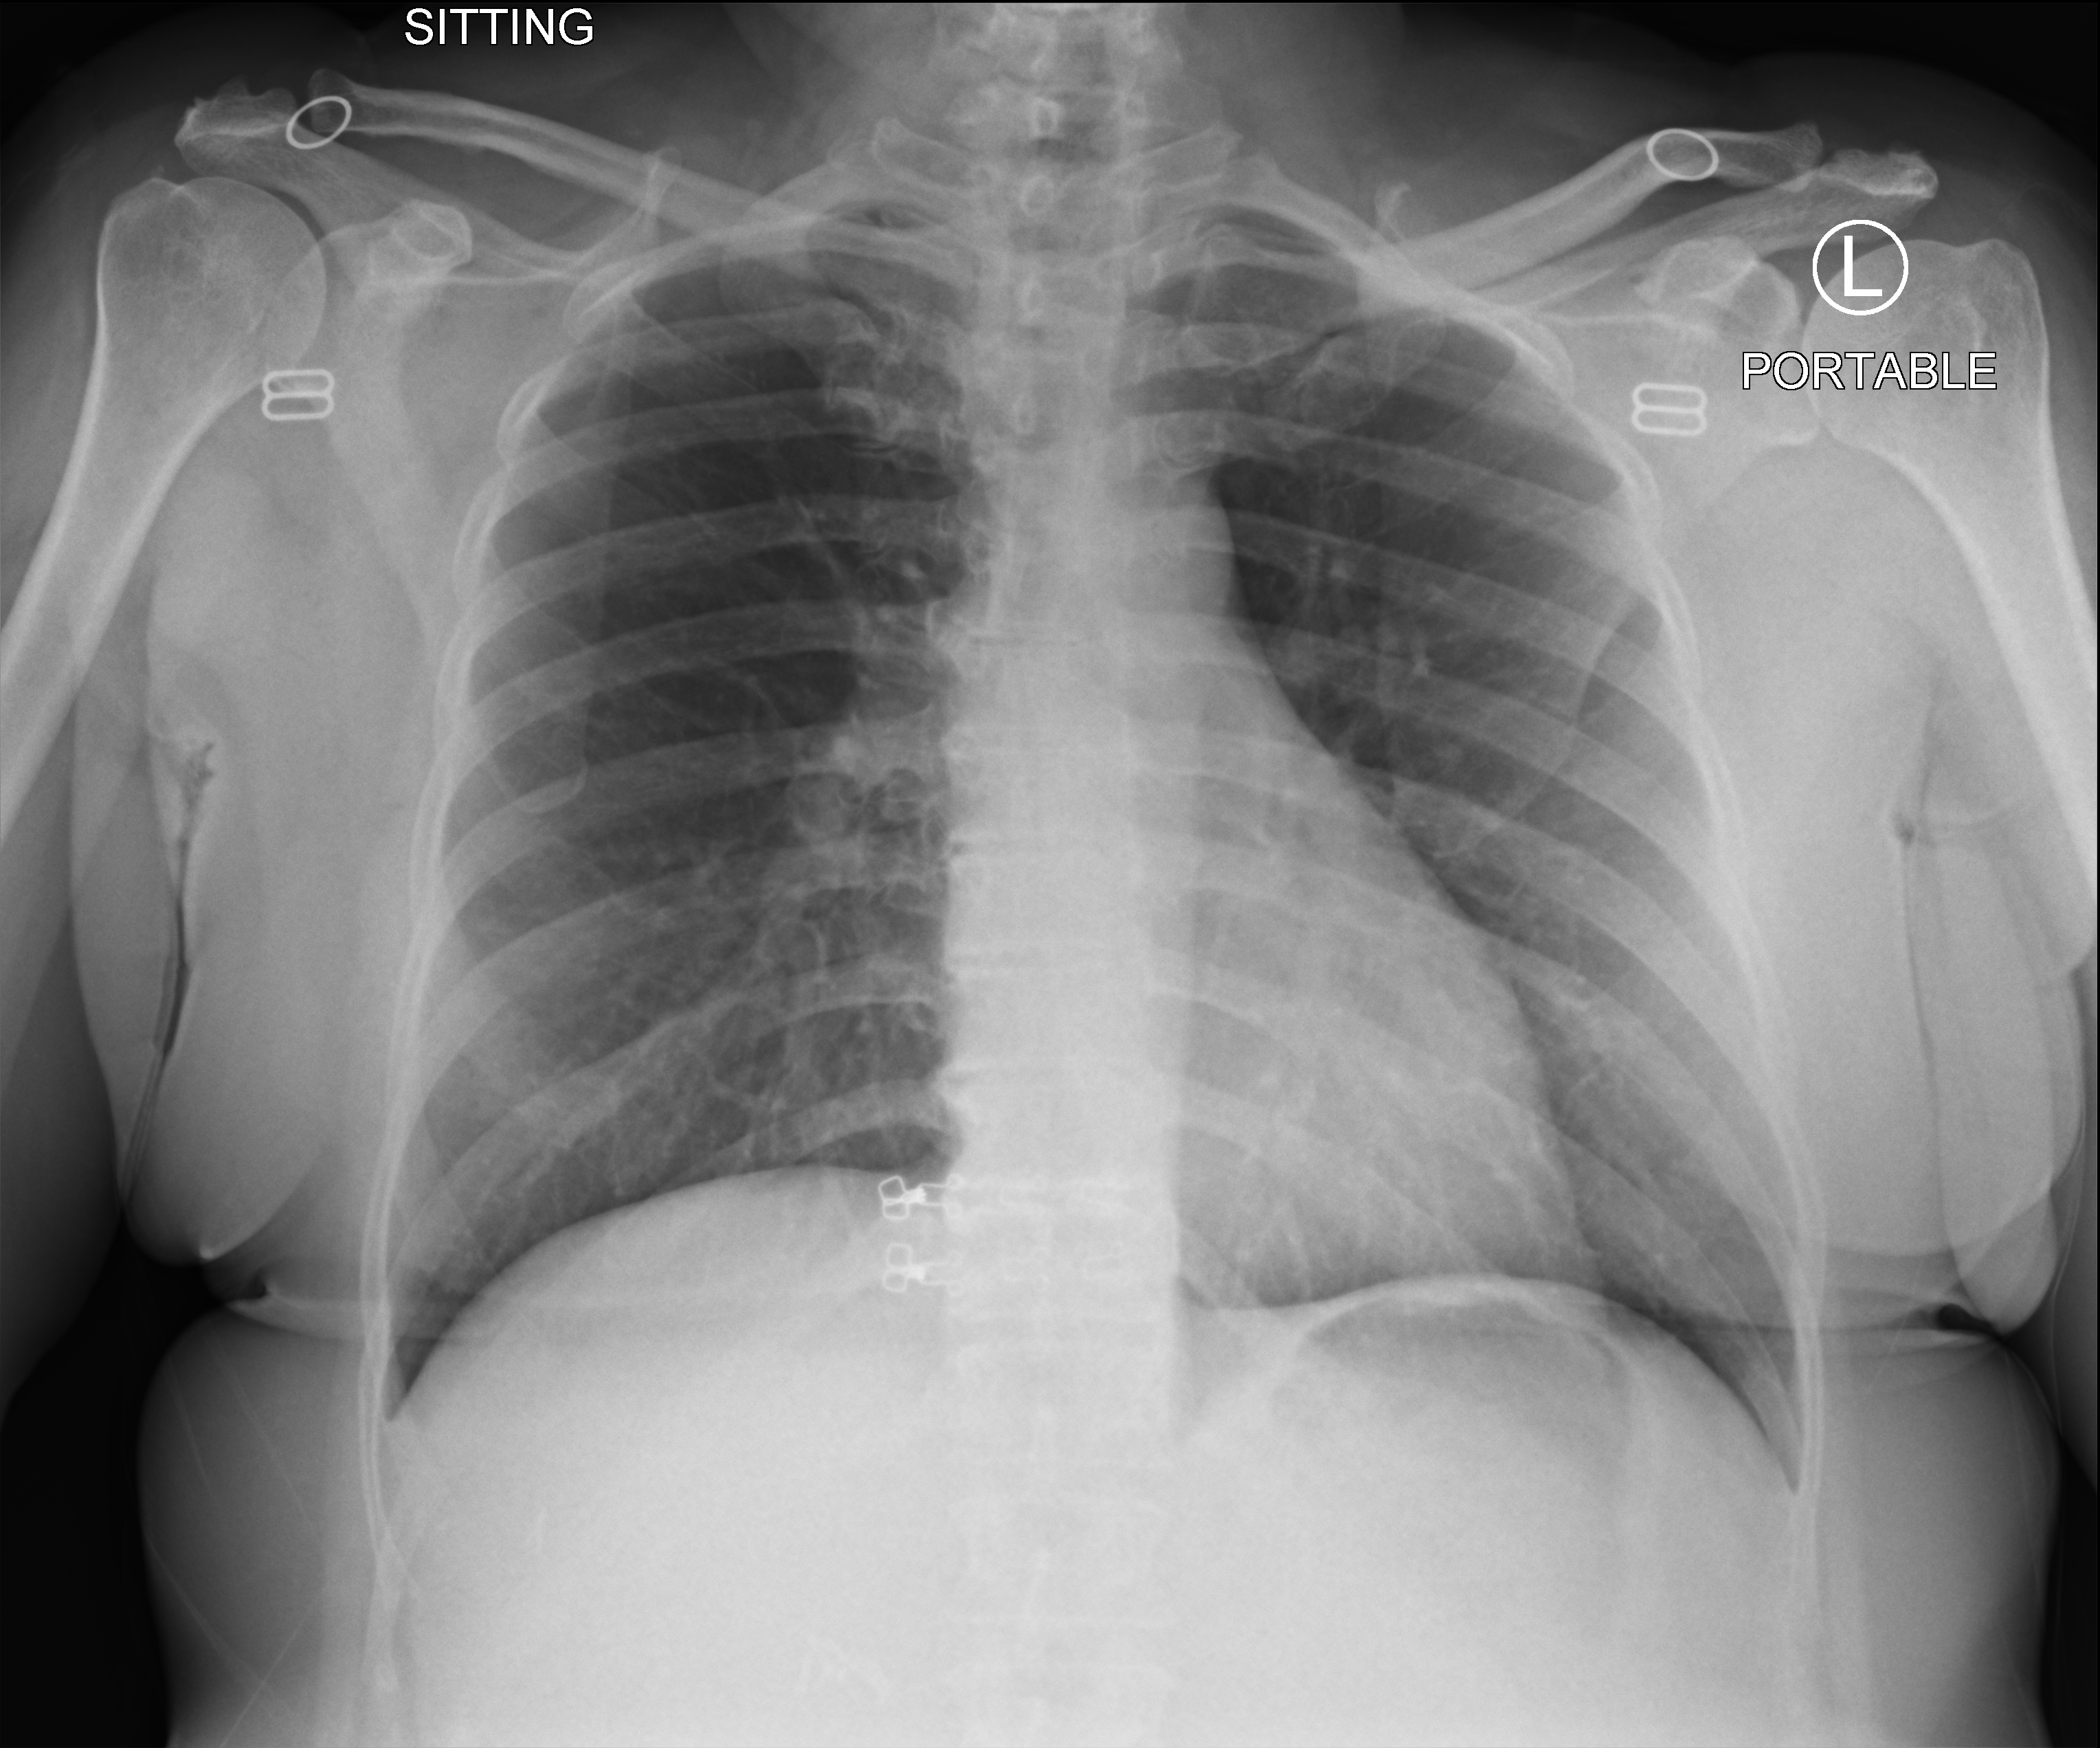
Portable chest radiograph; anteroposterior (AP) projection. Patient hospitalised with COVID-19; female, aged 18–59 years.
Admission-level facts for this patient (not findings on this image; timing relative to this image not recorded):
- length of hospital stay: 1 day